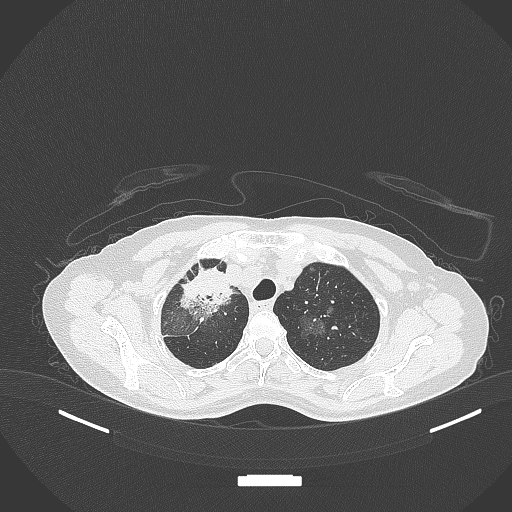
Chest CT, one axial slice; position 270 of 284 along the scan axis; reconstruction kernel B70f; 120 kVp; lung window (W 1500 / L -600 HU); 512 × 512 image matrix. Female patient, age 59 years. From the clinical record (not read from this slice): clinical TNM (as recorded): T3 N0 M0; histopathological grade: G1.
Structures marked on this image (bounding box drawn by a radiologist):
- lung tumour (recorded histology: adenocarcinoma): bounding box (x1, y1, x2, y2) in pixels: (177, 265, 236, 322)